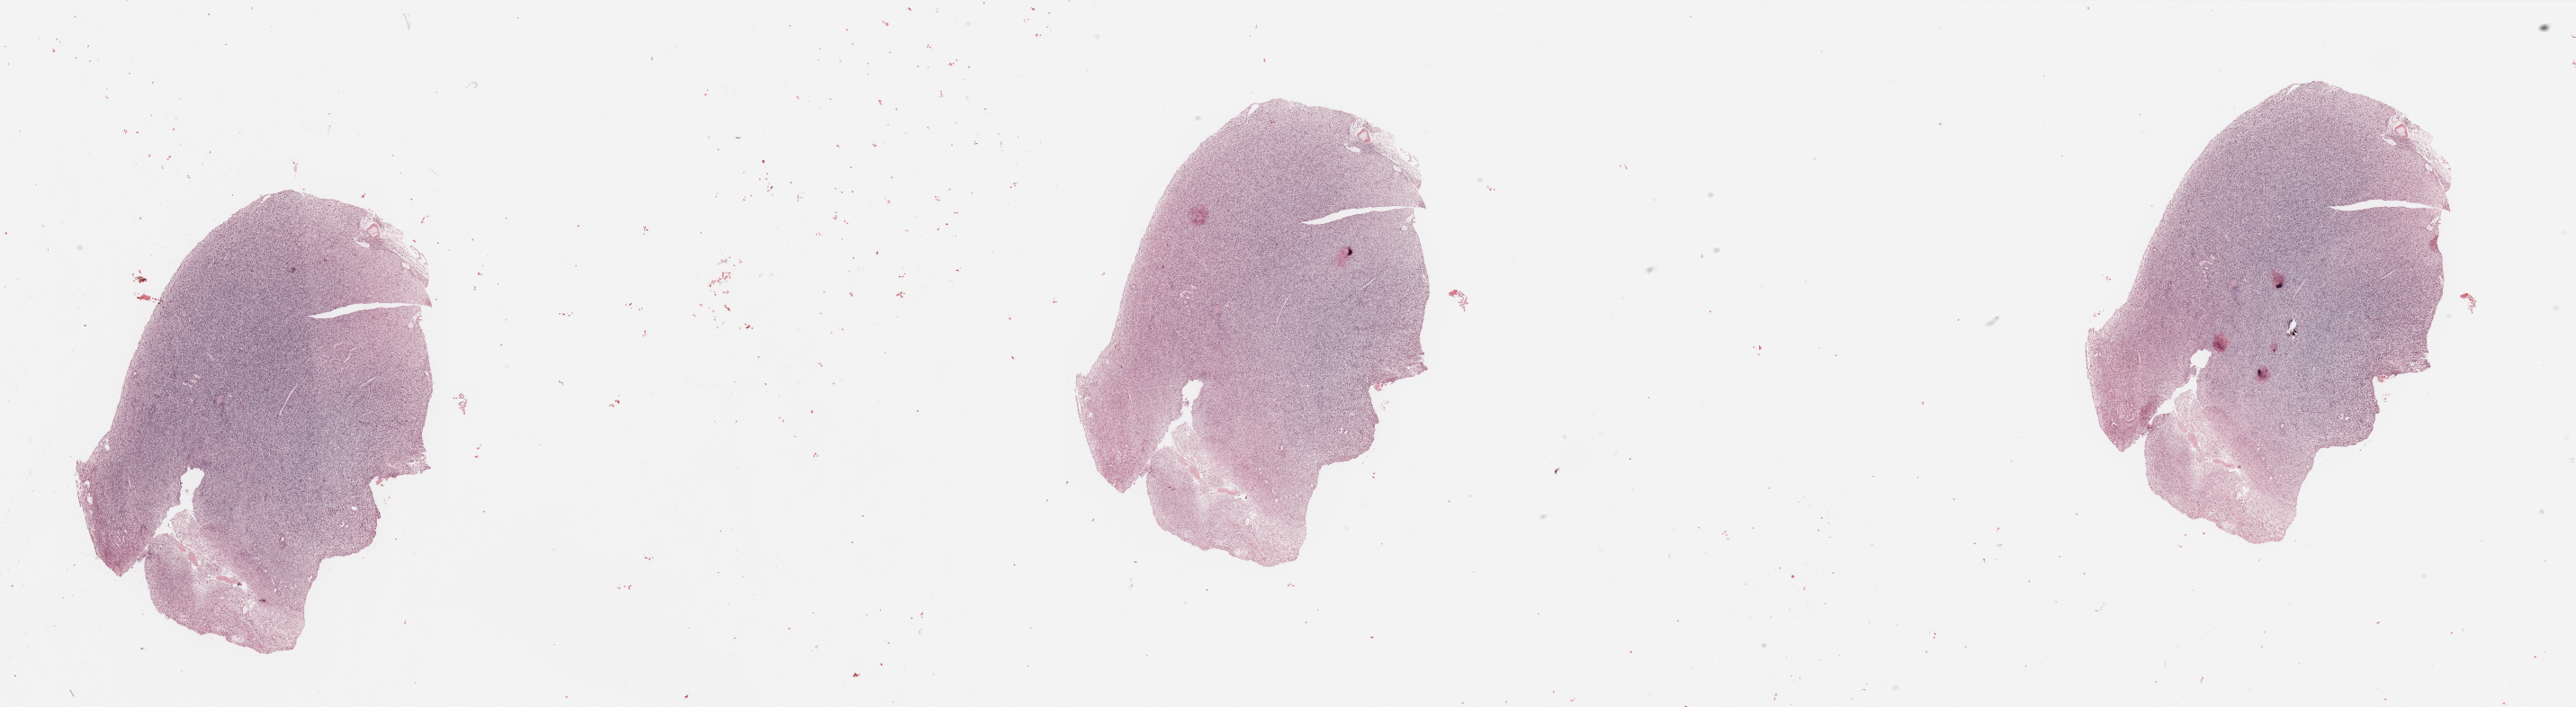
Digitized H&E tissue section (whole slide) — a low-resolution overview of the entire scanned area, about 45.3 x 12.4 mm. Tumour tissue sample, sampled site: frontal lobe. Male, 70 y/o. Composition of this section per pathologist review: tumour nuclei 95%, necrosis 3%.
Histologic diagnosis: Glioblastoma. Primary tumour site (as recorded): frontal lobe.